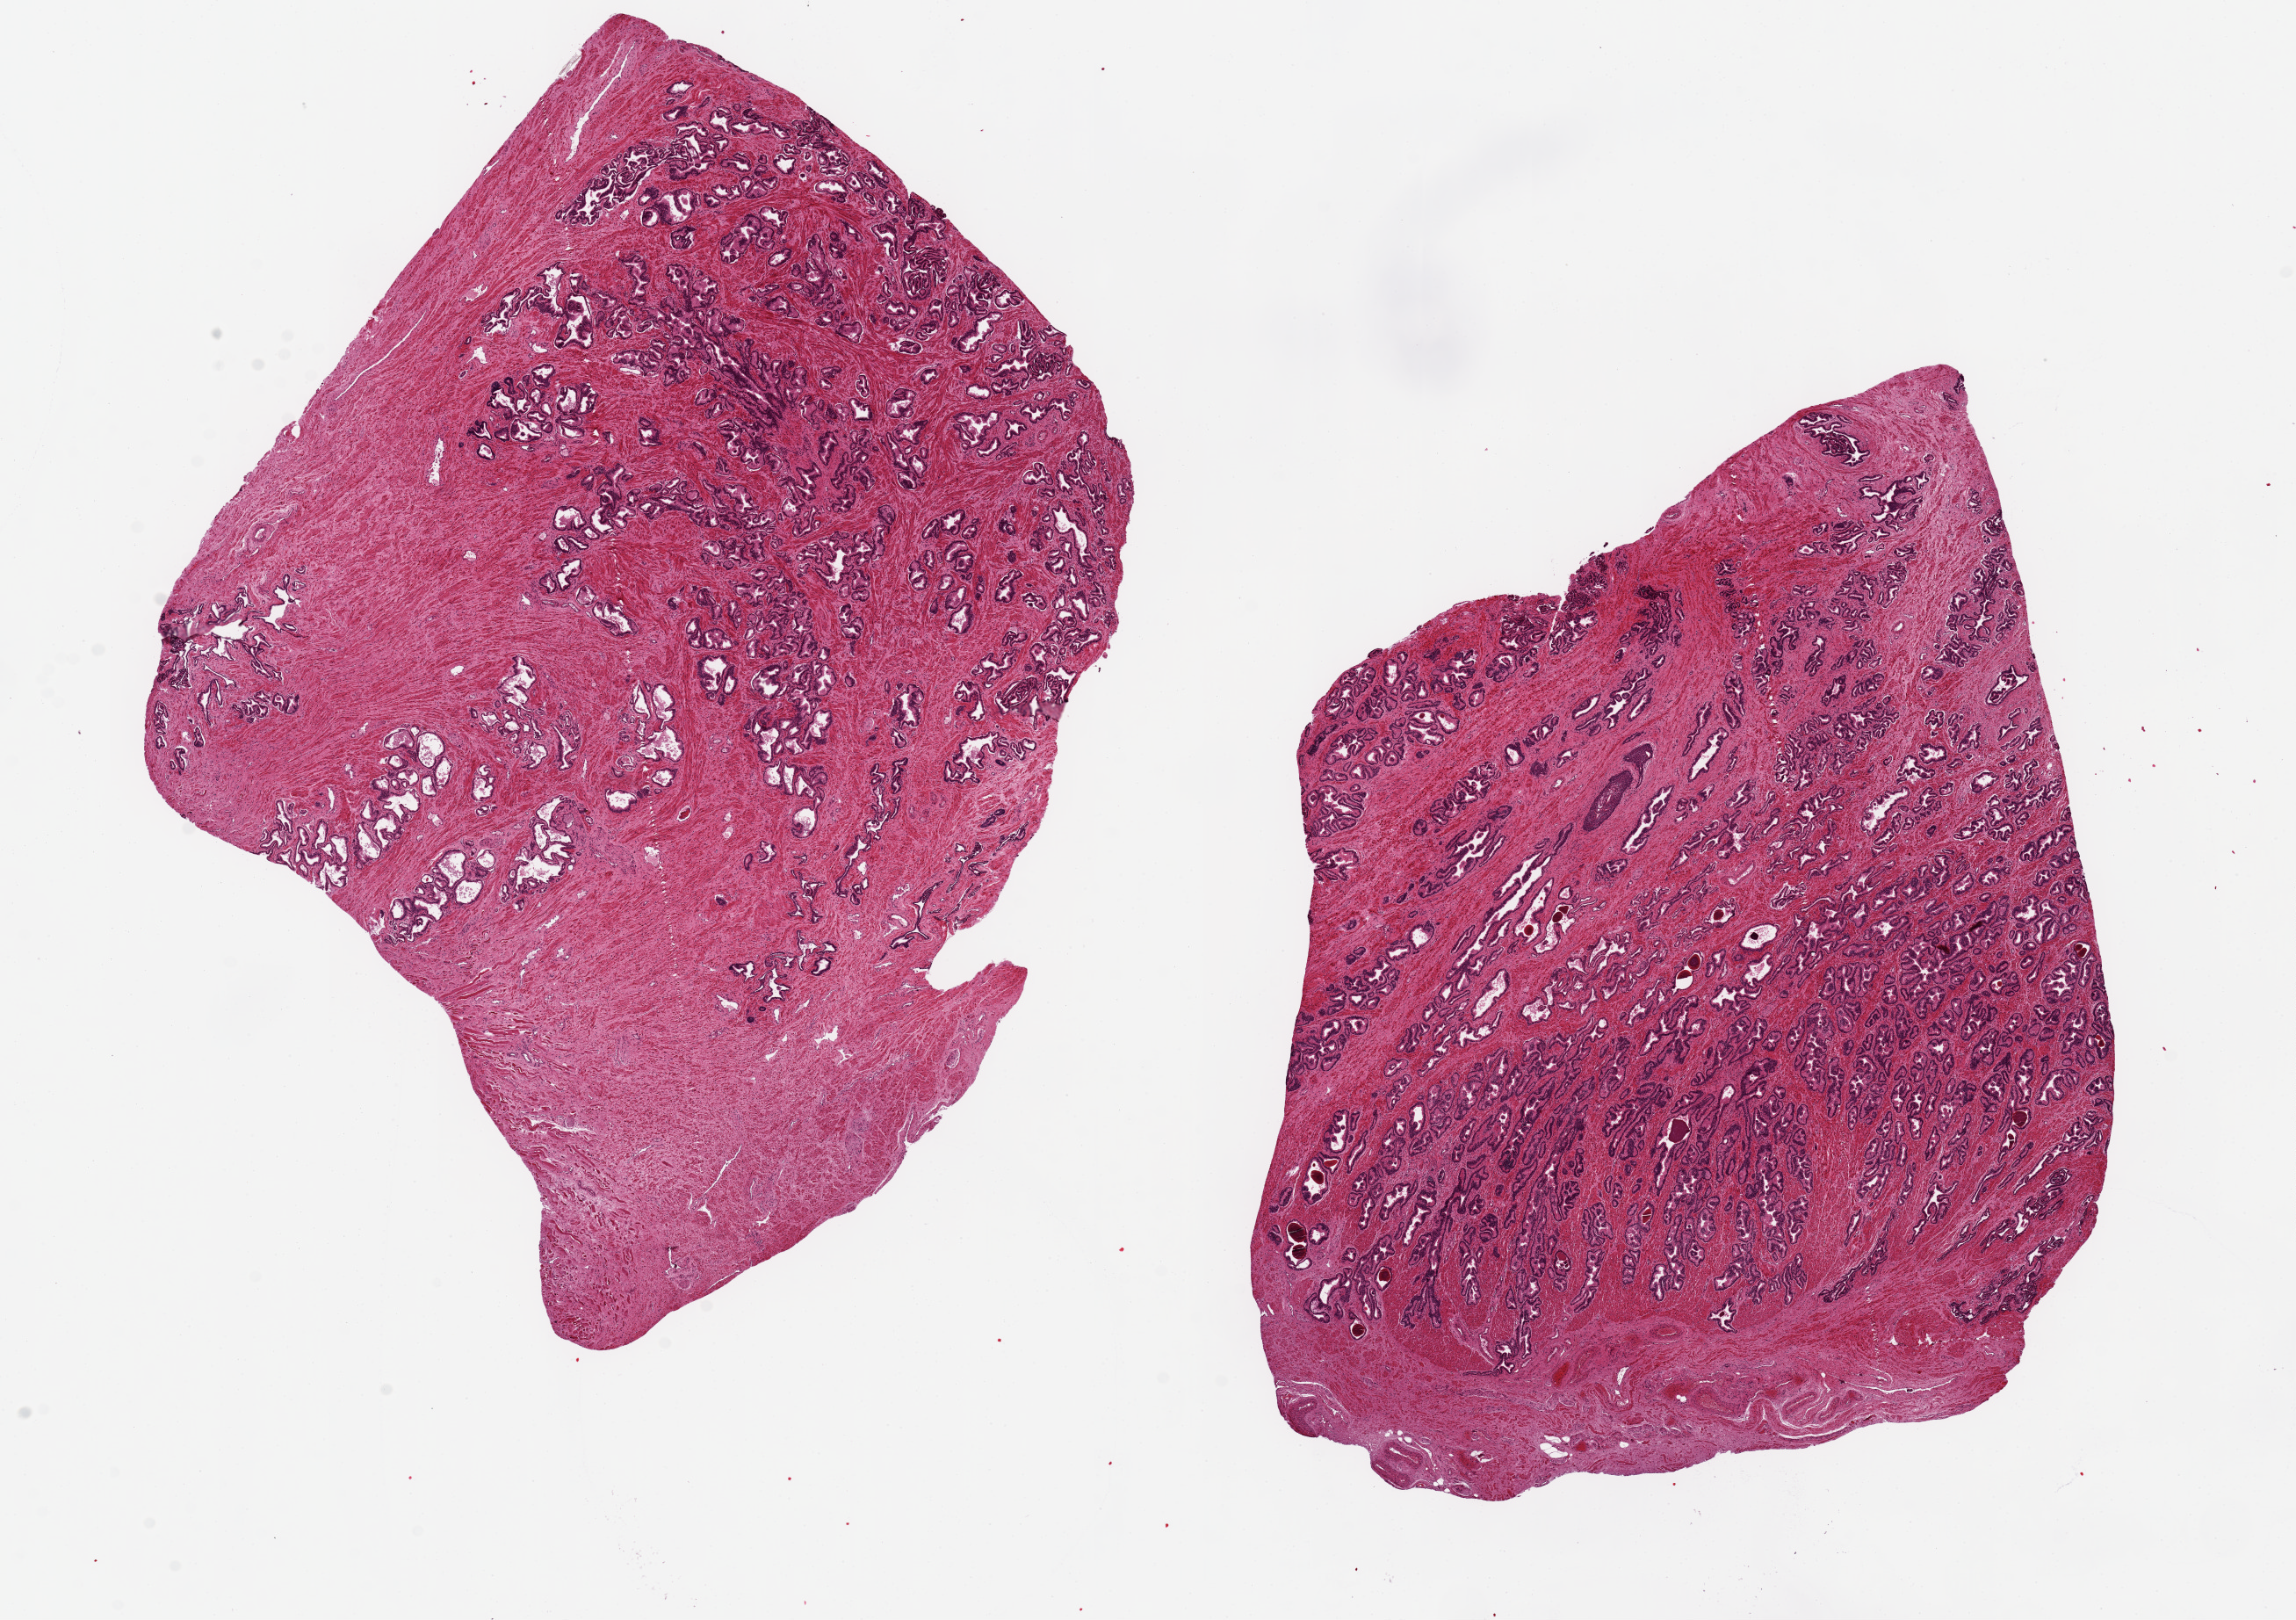
Digitized hematoxylin and eosin (H&E)-stained section, shown as a low-resolution overview of the whole scanned area (about 20.7 x 14.6 mm, slide scanned at 20x), PAXgene-fixed paraffin-embedded (PFPE) section, sampled site (target tissue): prostate, tissue donor sample. Donor sex: male.
• pathologist's review note for this sample: 2 ~8x8mm aliquots. Glandular hyperplasia